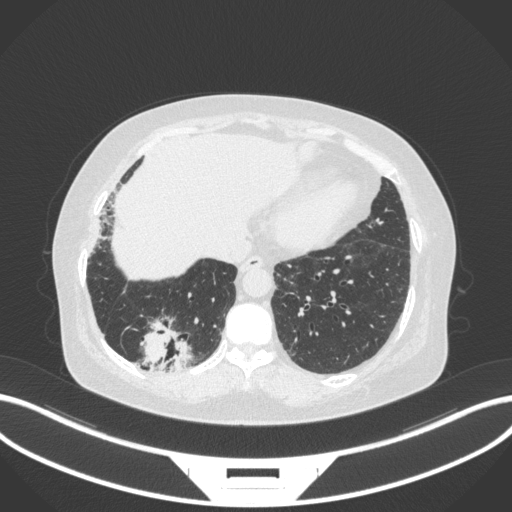
Chest CT, one axial slice; position 44 of 303 along the scan axis; 120 kVp; lung window (W 1500 / L -600 HU); 1 mm slice thickness; 512 × 512 image matrix, field of view 400 × 400 mm. Female patient, age 65 years. From the clinical record (not read from this slice): clinical TNM (as recorded): T2b N1 M0; histopathological grade: G1.
Outlined on this slice (bounding box drawn by a radiologist):
- lung tumour (recorded histology: adenocarcinoma): bounding box [x1, y1, x2, y2] px = [133, 313, 193, 373]